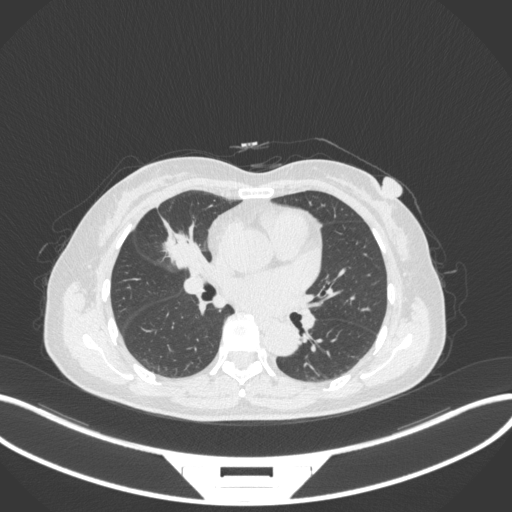
Chest CT, one axial slice. Position 156 of 282 along the scan axis. Reconstruction kernel B31f. Lung window (W 1500 / L -600 HU). 1 mm slice thickness. 512 × 512 image matrix, field of view 400 × 400 mm. Patient: female, 51 years. From the clinical record (not read from this slice): clinical TNM (as recorded): T1c N0 M0.
Annotated regions visible in this slice (bounding box drawn by a radiologist):
- lung tumour (recorded histology: adenocarcinoma): bounding box [x1, y1, x2, y2] px = [155, 216, 207, 274]